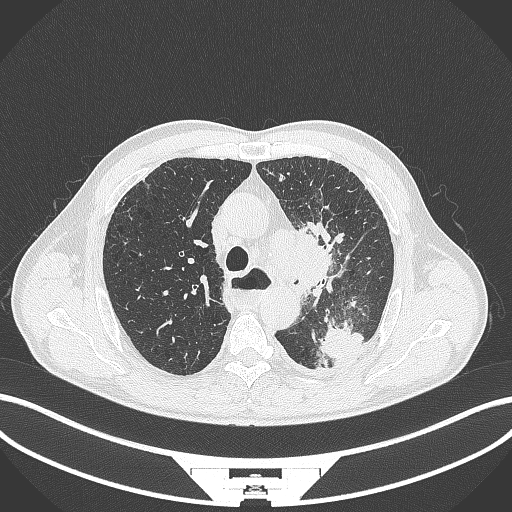
Chest CT, one axial slice. Slice 275 of 411 in the series (ordered by position). Reconstruction kernel B70f. 120 kVp. Lung window (W 1500 / L -600 HU). 1 mm slice thickness. 512 × 512 image matrix, field of view 400 × 400 mm. Patient: male, 57 years. Case-level facts recorded for this patient, not image findings: clinical TNM (as recorded): T2a N1 M0.
Annotated regions visible in this slice (rectangle marked by the reading radiologist):
- lung tumour (recorded histology: squamous cell carcinoma): bounding box <287,224,340,300> (left, top, right, bottom; pixels)